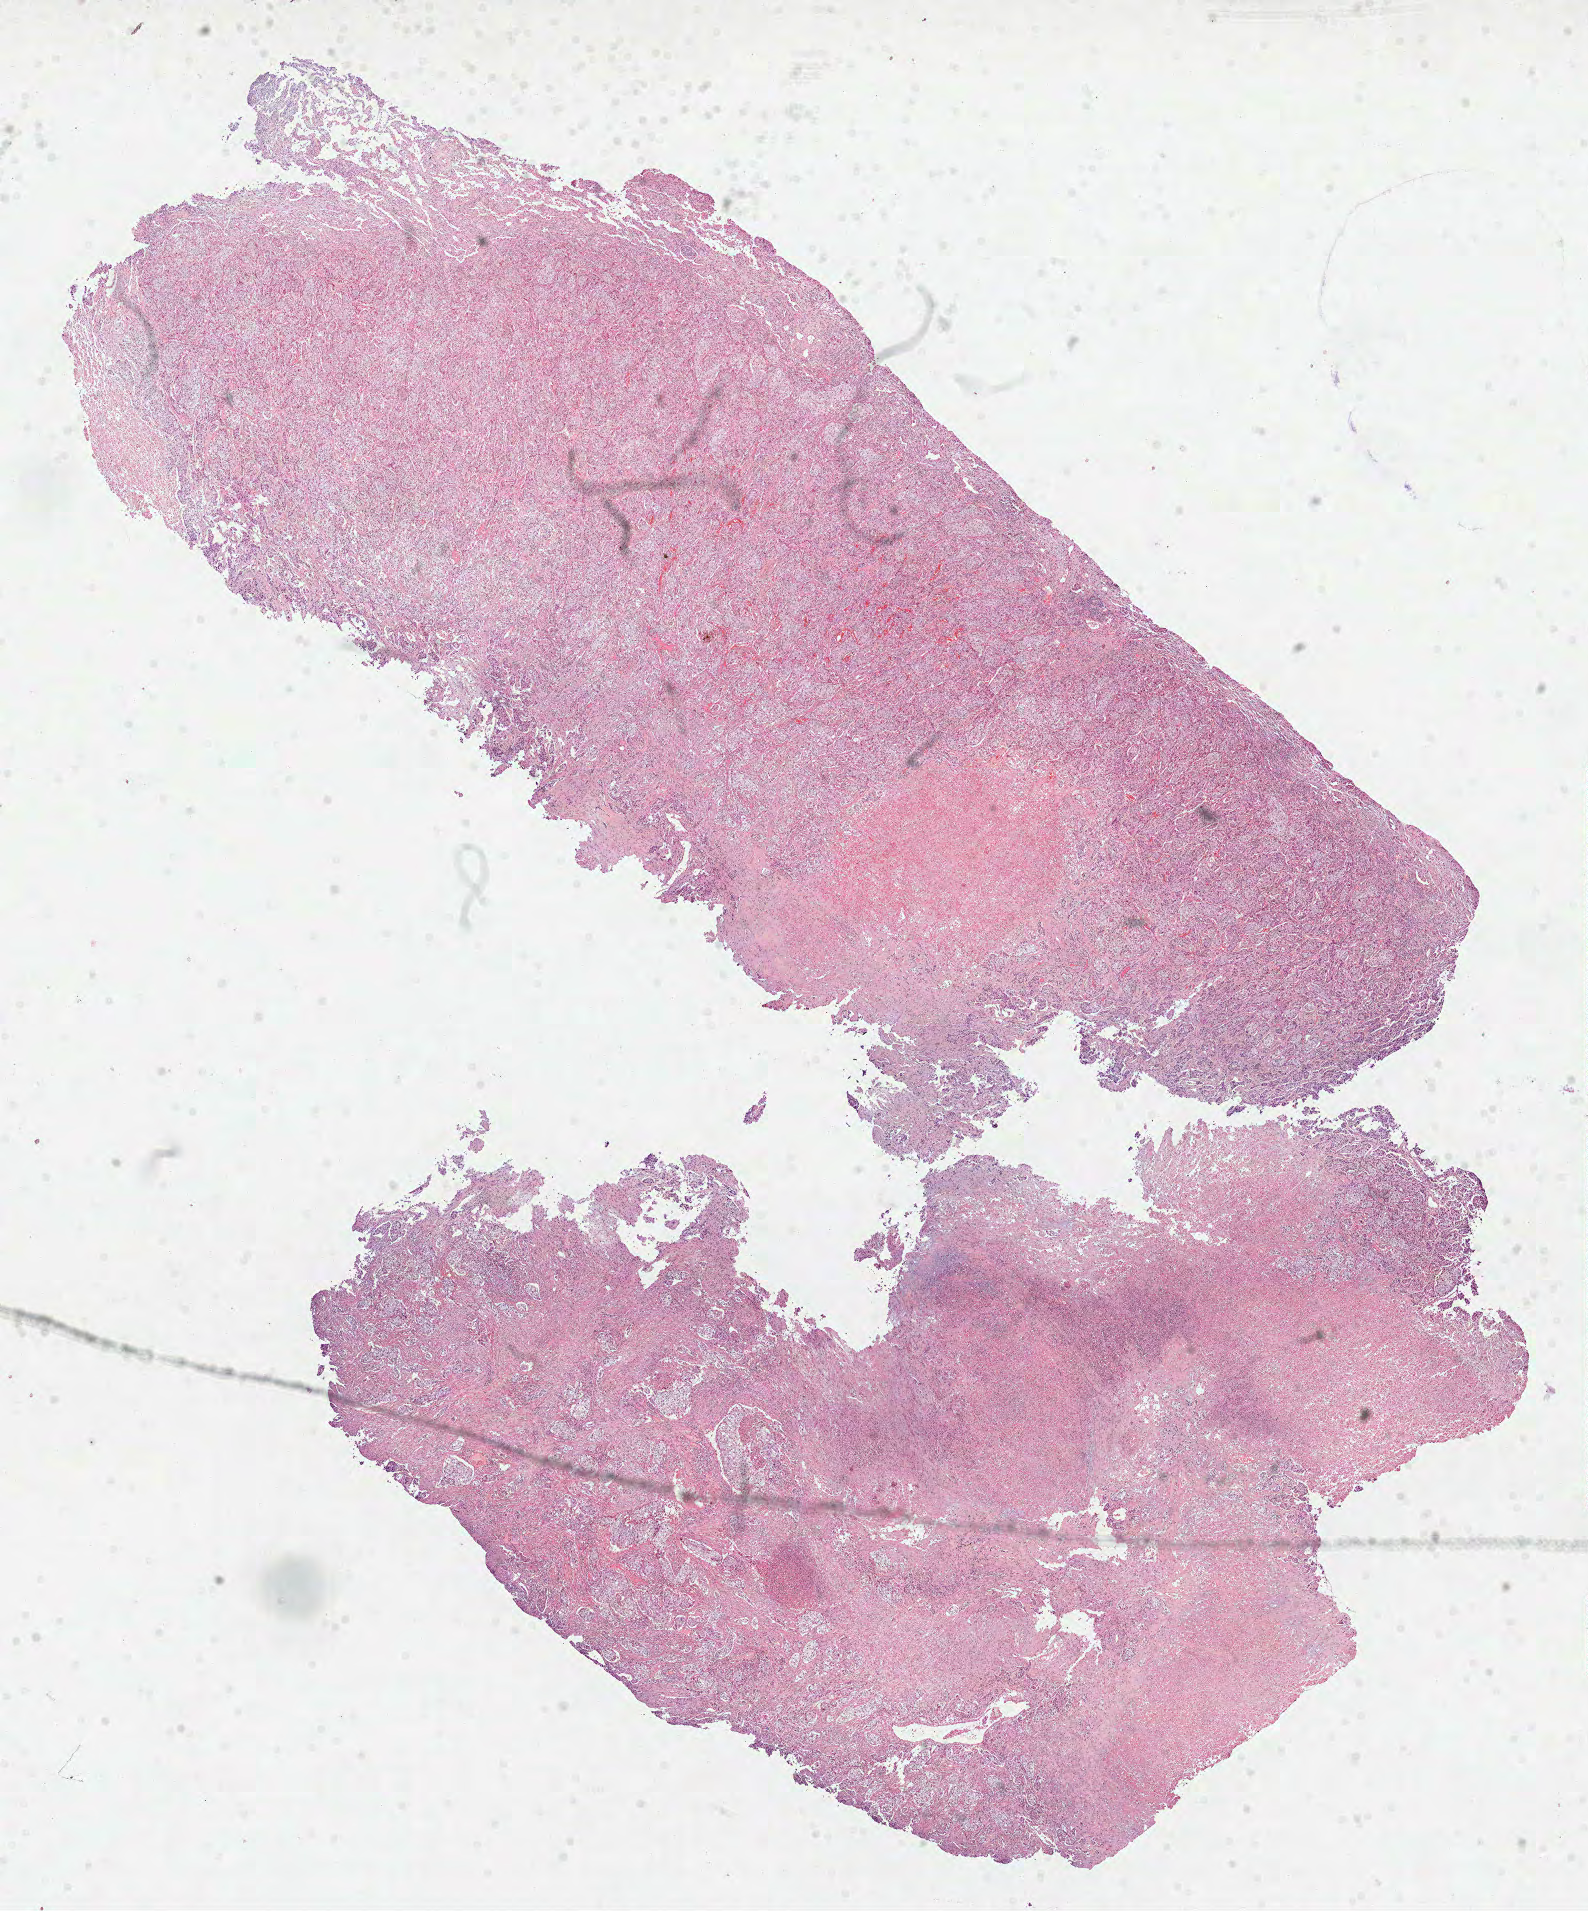
H&E-stained whole-slide image, shown as a low-resolution overview of the whole scanned area (about 12.8 x 15.4 mm). FFPE section. Primary tumour sample from the lung. Patient: male, age at initial diagnosis 73 years.
Laterality: right. Pathologic diagnosis: Squamous cell carcinoma, NOS. AJCC pathologic stage: IB.